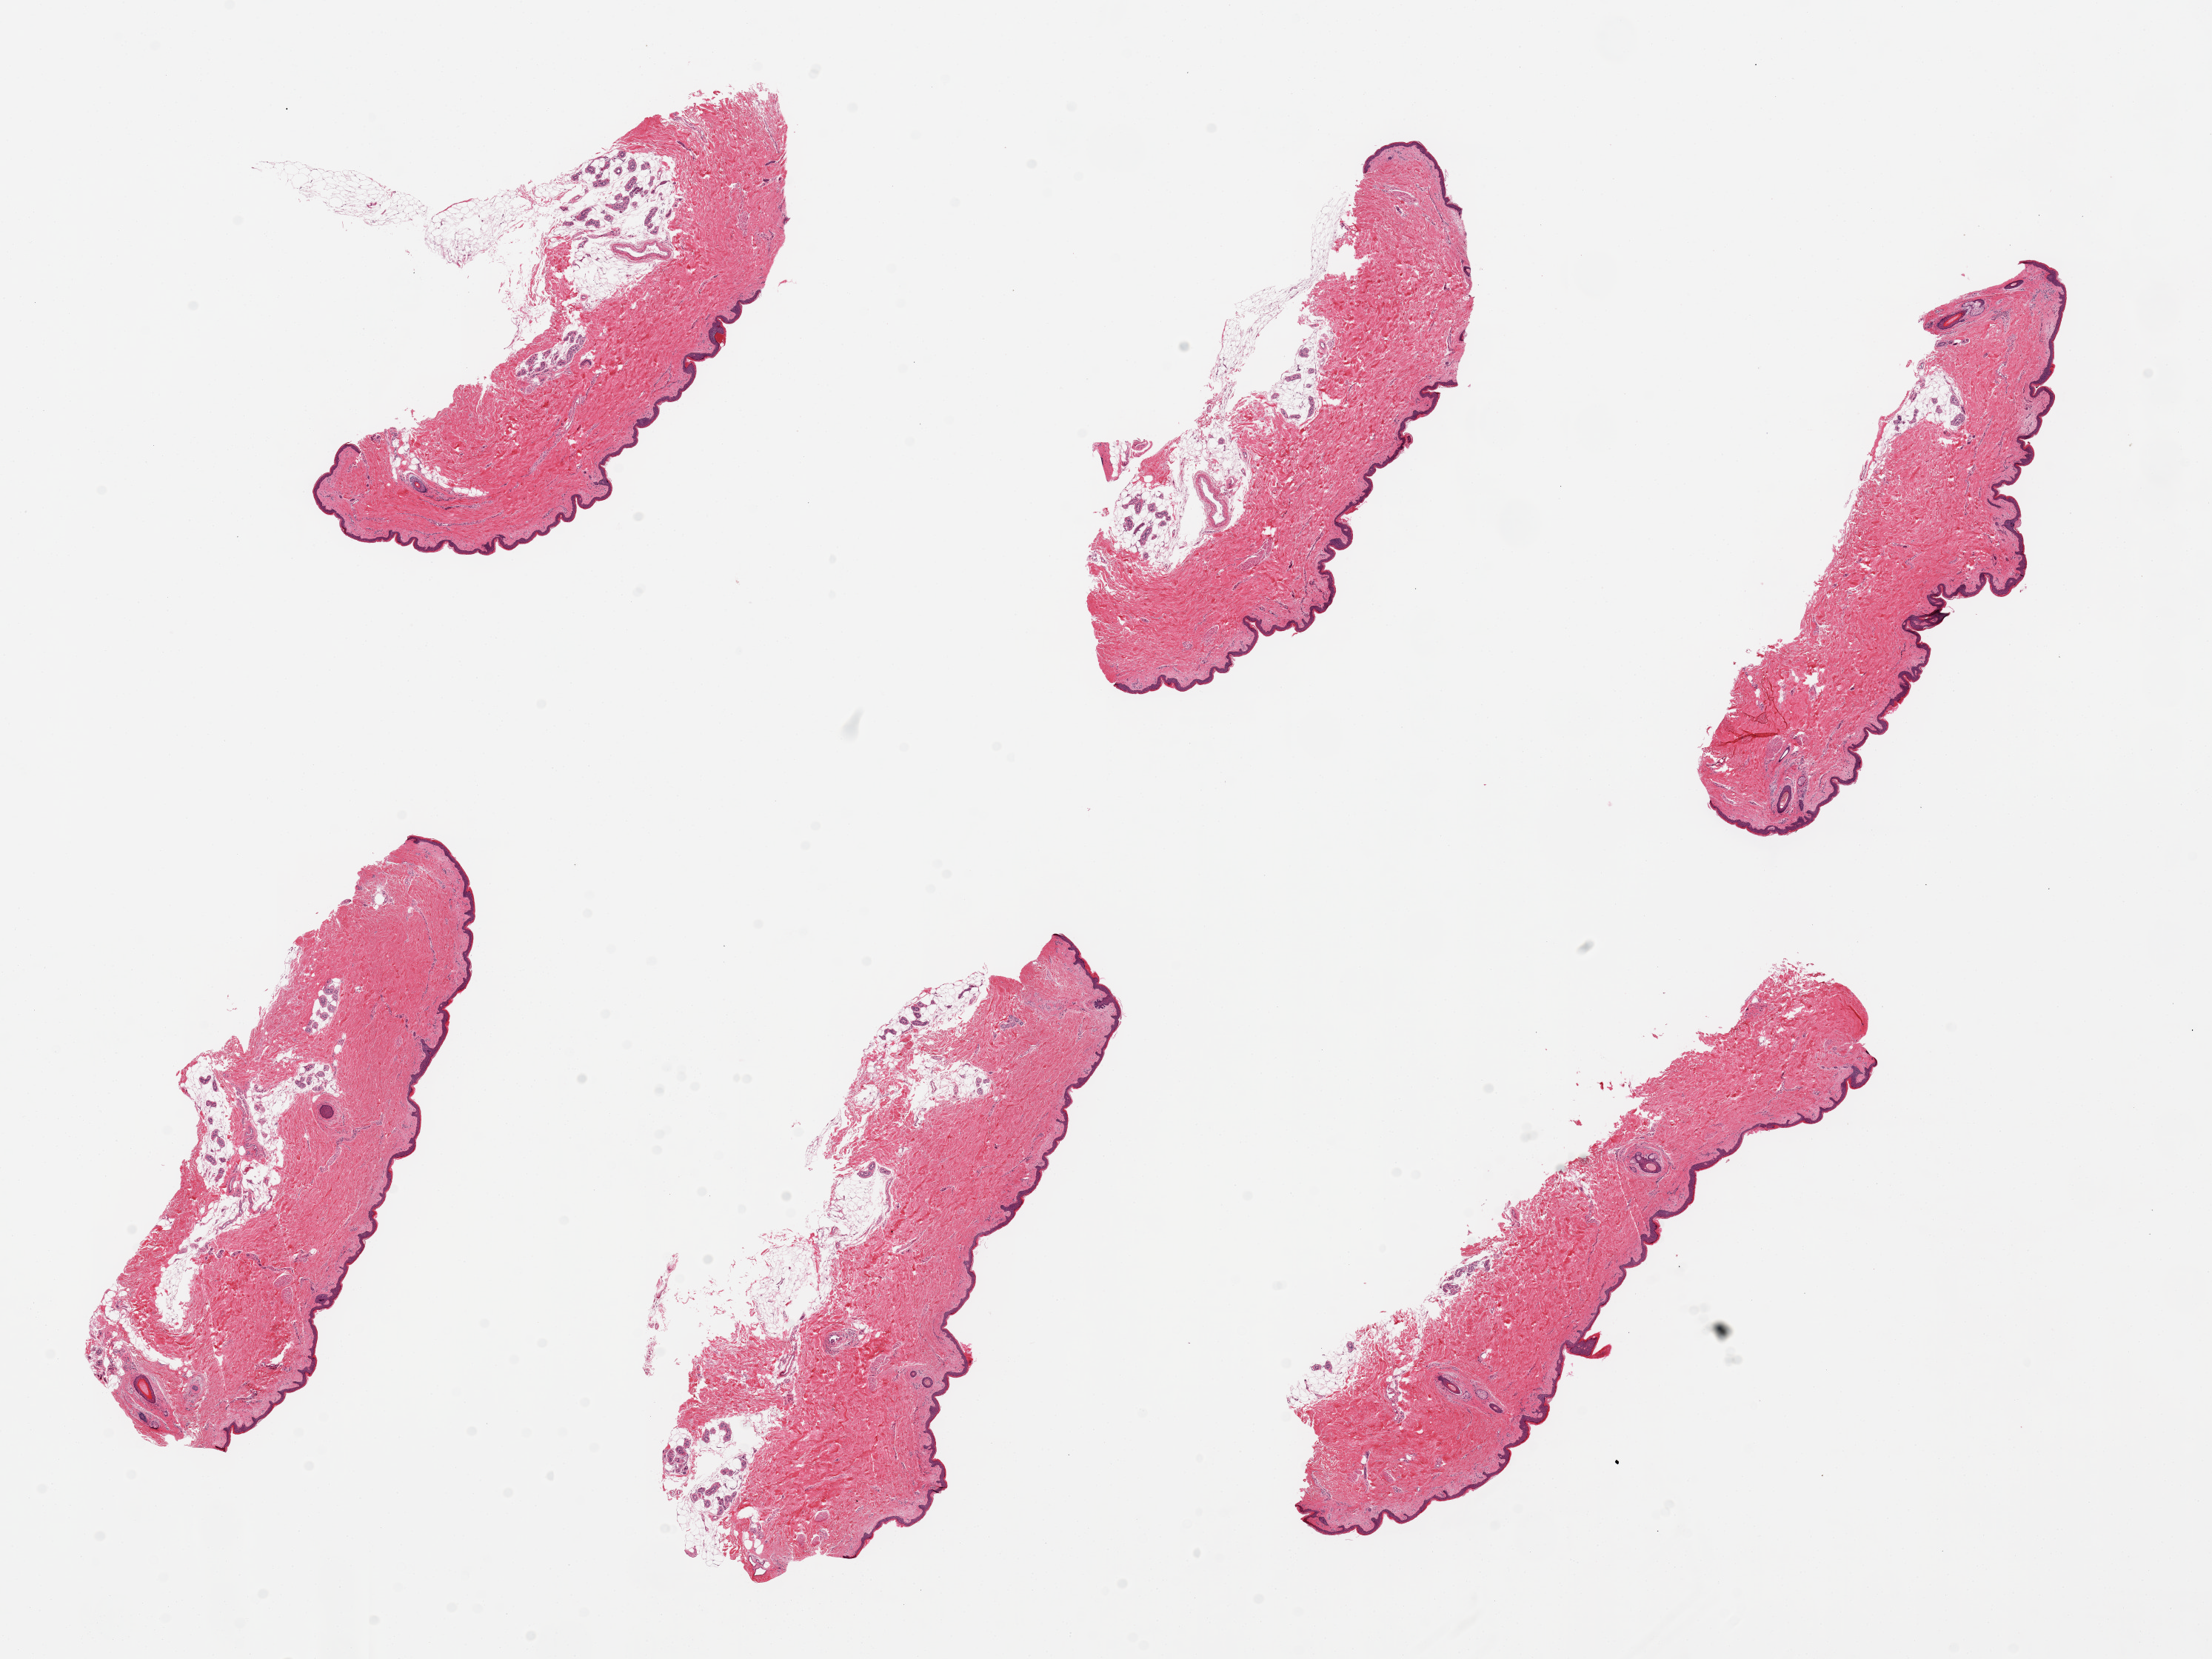
Hematoxylin and eosin (H&E) whole-slide image, shown as a low-resolution overview of the whole scanned area (about 23.6 x 17.7 mm). PAXgene-fixed paraffin-embedded (PFPE) section. Target tissue: skin of suprapubic region. Tissue donor sample. Female donor.
- review note (as recorded): 6 pieces. up to 8x4mm; focal subcutaneous adipose with embedded sweat glands